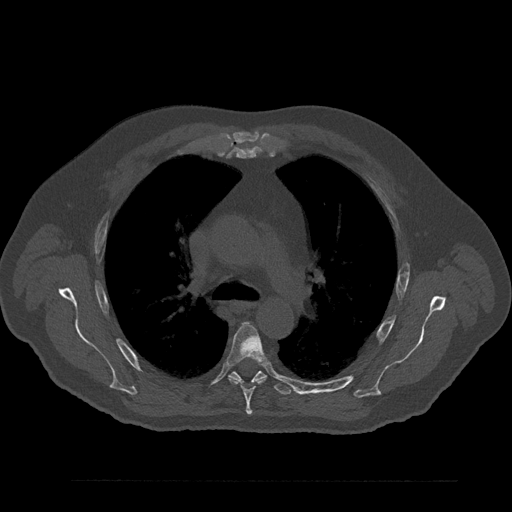
CT including the spine, one axial slice. Slice 588 of 797 in the series (ordered by position). Reconstruction kernel Br40s/3. Bone window (W 1800 / L 400 HU). 0.5 mm slice thickness. 512 × 512 image matrix, field of view 430 × 430 mm. Patient: male, 61 years. Case-level facts recorded for this patient, not image findings: primary cancer: prostate.
Annotated regions visible in this slice (semi-automatically segmented with operator editing):
- T5 vertebra: bounding box (x1, y1, x2, y2) in pixels: (226, 323, 266, 415)
- T6 vertebra: (229, 364, 292, 395)